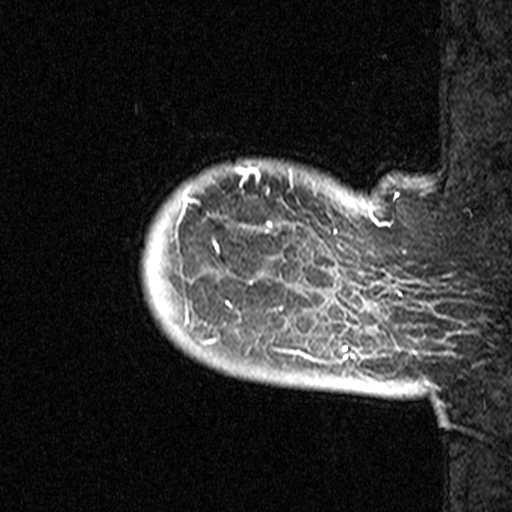
Breast MRI (dynamic contrast-enhanced), one sagittal slice. Slice 3 of 44 in the series (ordered by position). Dynamic contrast-enhanced study with each time point stored as its own series, time point 2 of 3 at this slice position (early post-contrast, ordered by acquisition time). 1.5 T. TE 4.5 ms, TR 11 ms. 3 mm slice thickness. 512 × 512 image matrix, field of view 200 × 200 mm. Patient: female, 53 years. From the clinical record (not read from this slice): setting: breast cancer imaged before/during neoadjuvant chemotherapy; receptor status: HR-positive, HER2-negative.
Structures marked on this image (semi-automatic segmentation, software-assisted and operator-edited):
- analysis volume of interest (the breast-tissue region the enhancement analysis was run in; not a lesion): bounding box [x1, y1, x2, y2] px = [140, 156, 311, 353]
- tumour enhancement mask (voxels above the 90 % enhancement threshold inside the analysis volume of interest): [197, 169, 272, 253]